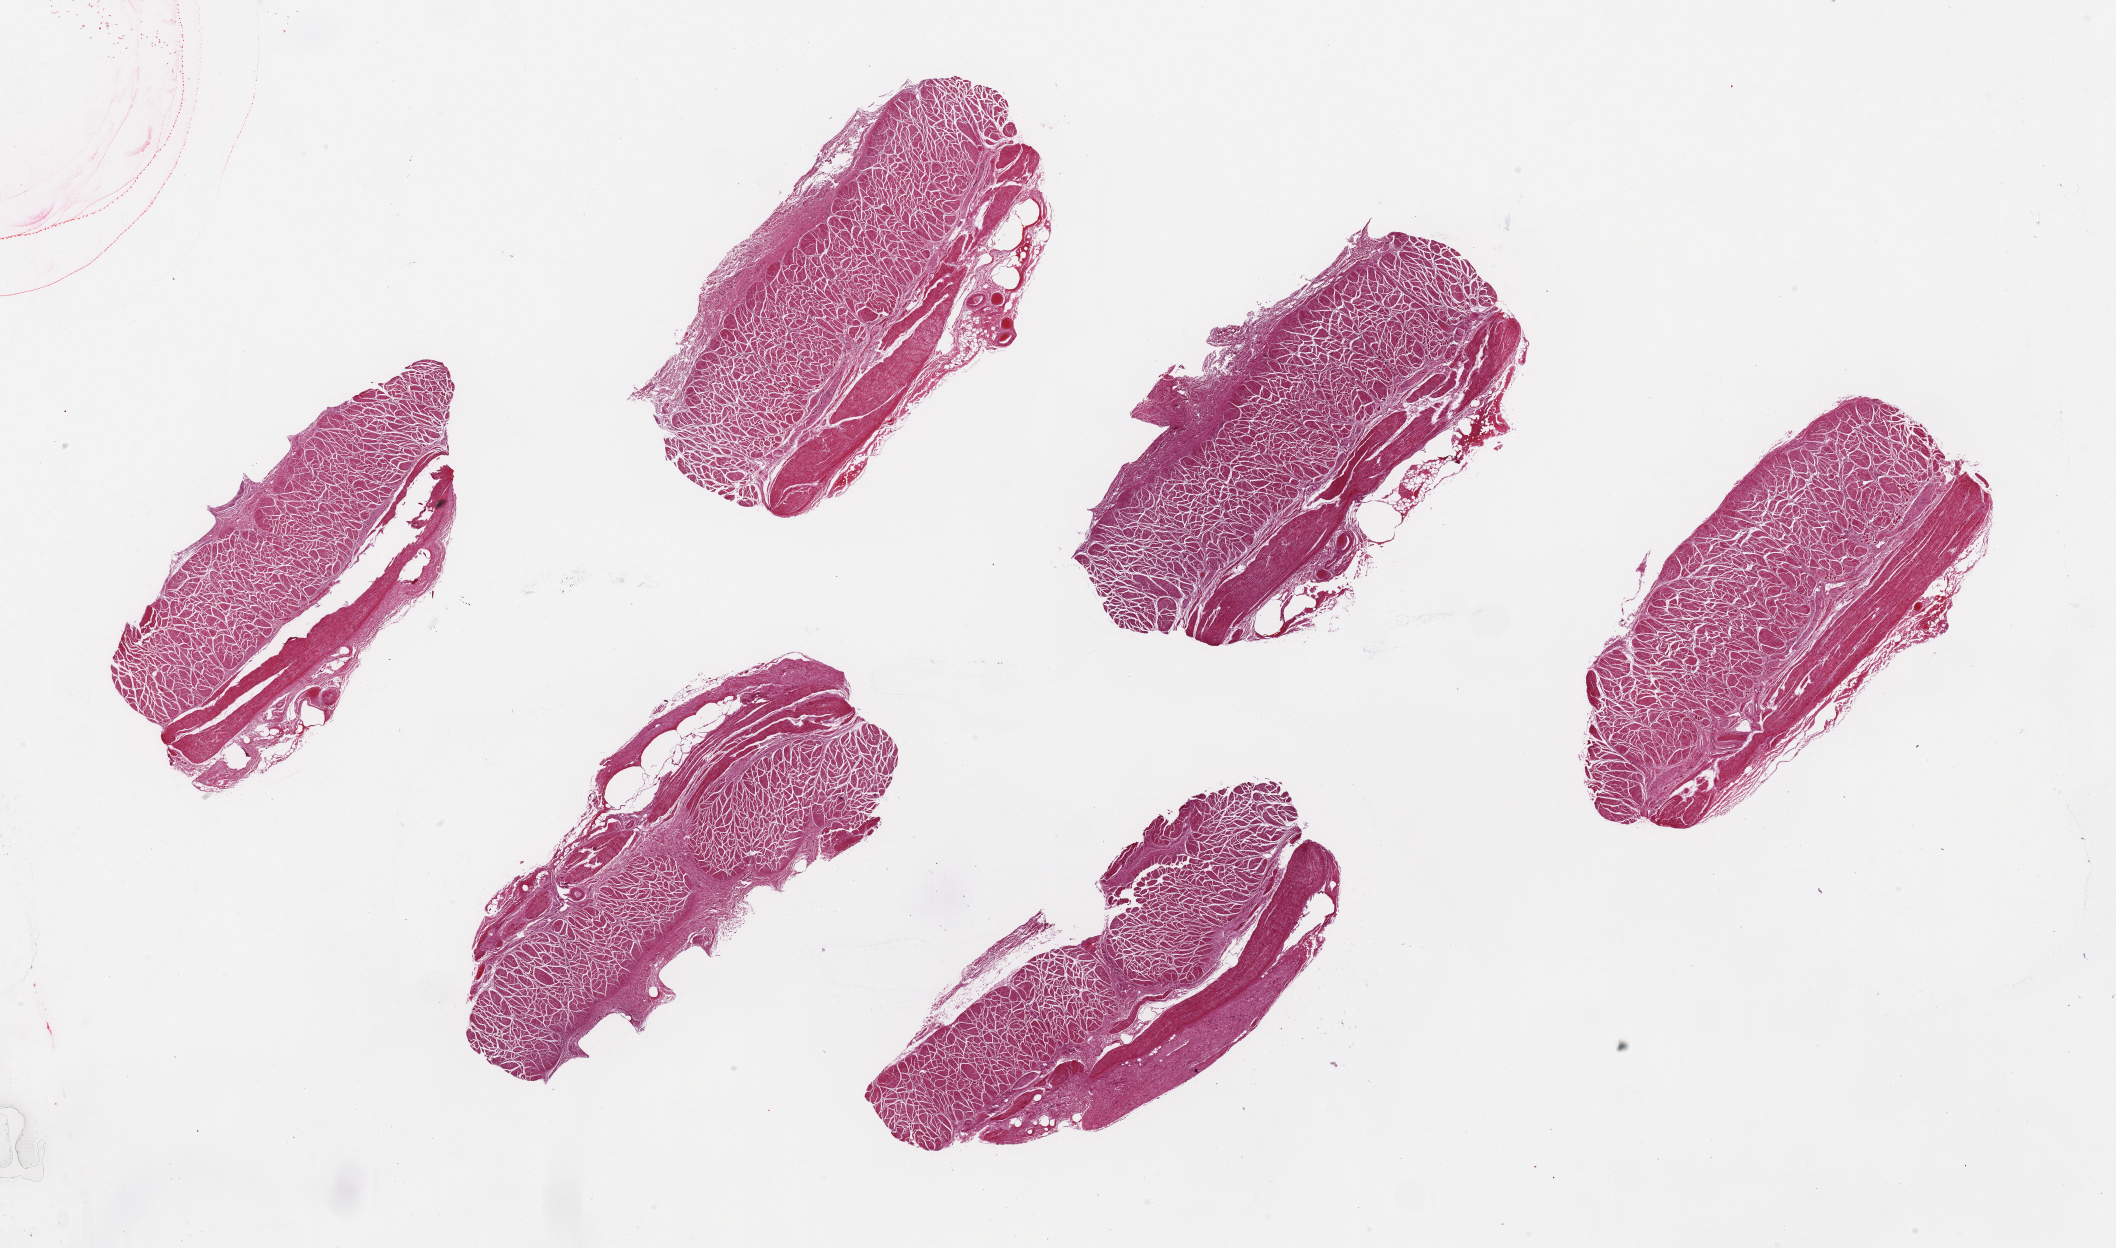
Whole-slide image, hematoxylin and eosin (H&E) stain — whole scanned area (about 33.5 x 19.7 mm, slide scanned at 20x) shown as a low-resolution overview, PAXgene-fixed, paraffin-embedded tissue, target tissue: esophageal muscle, tissue donor sample. Donor sex: female.
Pathologist's review note for this sample: 6 pieces, 8x4mm.